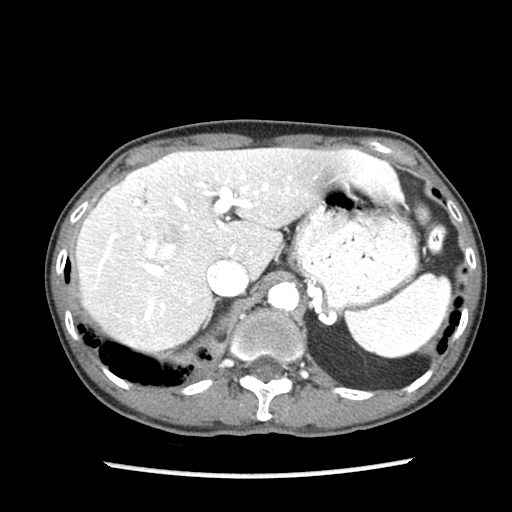
Contrast-enhanced abdominal CT (liver protocol), one axial slice. Slice 61 of 87 in the series (ordered by position). 140 kVp. Soft-tissue window (W 400 / L 40 HU). 512 × 512 image matrix, field of view 300 × 300 mm. Case-level facts recorded for this patient, not image findings: diagnosis: hepatocellular carcinoma (patient treated with transarterial chemoembolisation; whether this scan precedes or follows treatment is not stated here); TNM stage (as recorded): Stage-IIIB; Child-Pugh class: A; tumour differentiation: well differentiated; tumour nodularity: uninodular.
Outlined on this slice (semi-automatic segmentation, software-assisted and operator-edited):
- liver parenchyma outside the tumour (the mass and vessels are separate outlines, so this box may not span the whole liver): bounding box <76,148,400,352> (left, top, right, bottom; pixels)
- mass: <144,233,177,262>
- liver vessels: <98,156,386,319>